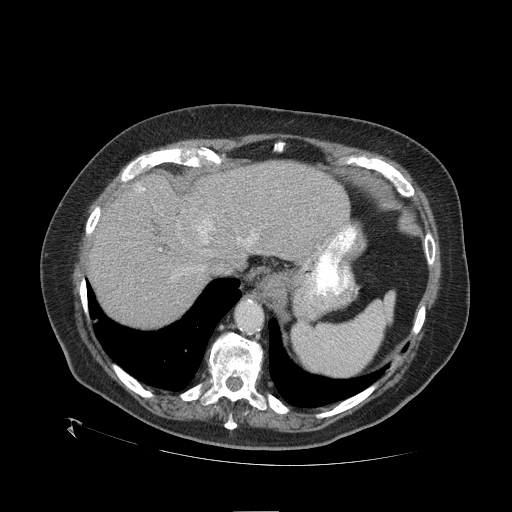
Contrast-enhanced abdominal CT (liver protocol), one axial slice; position 87 of 109 along the scan axis; reconstruction kernel STANDARD; one of 2 acquisitions stored at this slice position; soft-tissue window (W 400 / L 40 HU); 2.5 mm slice thickness; 512 × 512 image matrix. Case-level facts recorded for this patient, not image findings: diagnosis: hepatocellular carcinoma (patient treated with transarterial chemoembolisation; whether this scan precedes or follows treatment is not stated here); TNM stage (as recorded): Stage-I; Child-Pugh class: A; tumour nodularity: uninodular; tumour size: 4.6 cm.
Structures marked on this image (semi-automatic segmentation, software-assisted and operator-edited):
- abdominal aorta: bounding box (x1, y1, x2, y2) in pixels: (238, 301, 263, 331)
- liver parenchyma outside the tumour (the mass and vessels are separate outlines, so this box may not span the whole liver): (88, 160, 350, 326)
- mass: (173, 203, 212, 247)
- liver vessels: (137, 185, 257, 250)